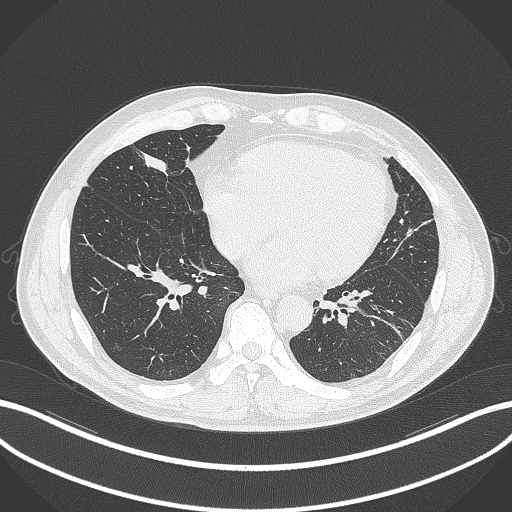
Chest CT, one axial slice. Slice 94 of 399 in the series (ordered by position). Reconstruction kernel B70f. 120 kVp. Lung window (W 1500 / L -600 HU). 1 mm slice thickness. 512 × 512 image matrix. Patient: male, 59 years. From the clinical record (not read from this slice): clinical TNM (as recorded): T2a N1 M0.
Structures marked on this image (rectangle marked by the reading radiologist):
- lung tumour (recorded histology: adenocarcinoma): bounding box <134,144,179,183> (left, top, right, bottom; pixels)